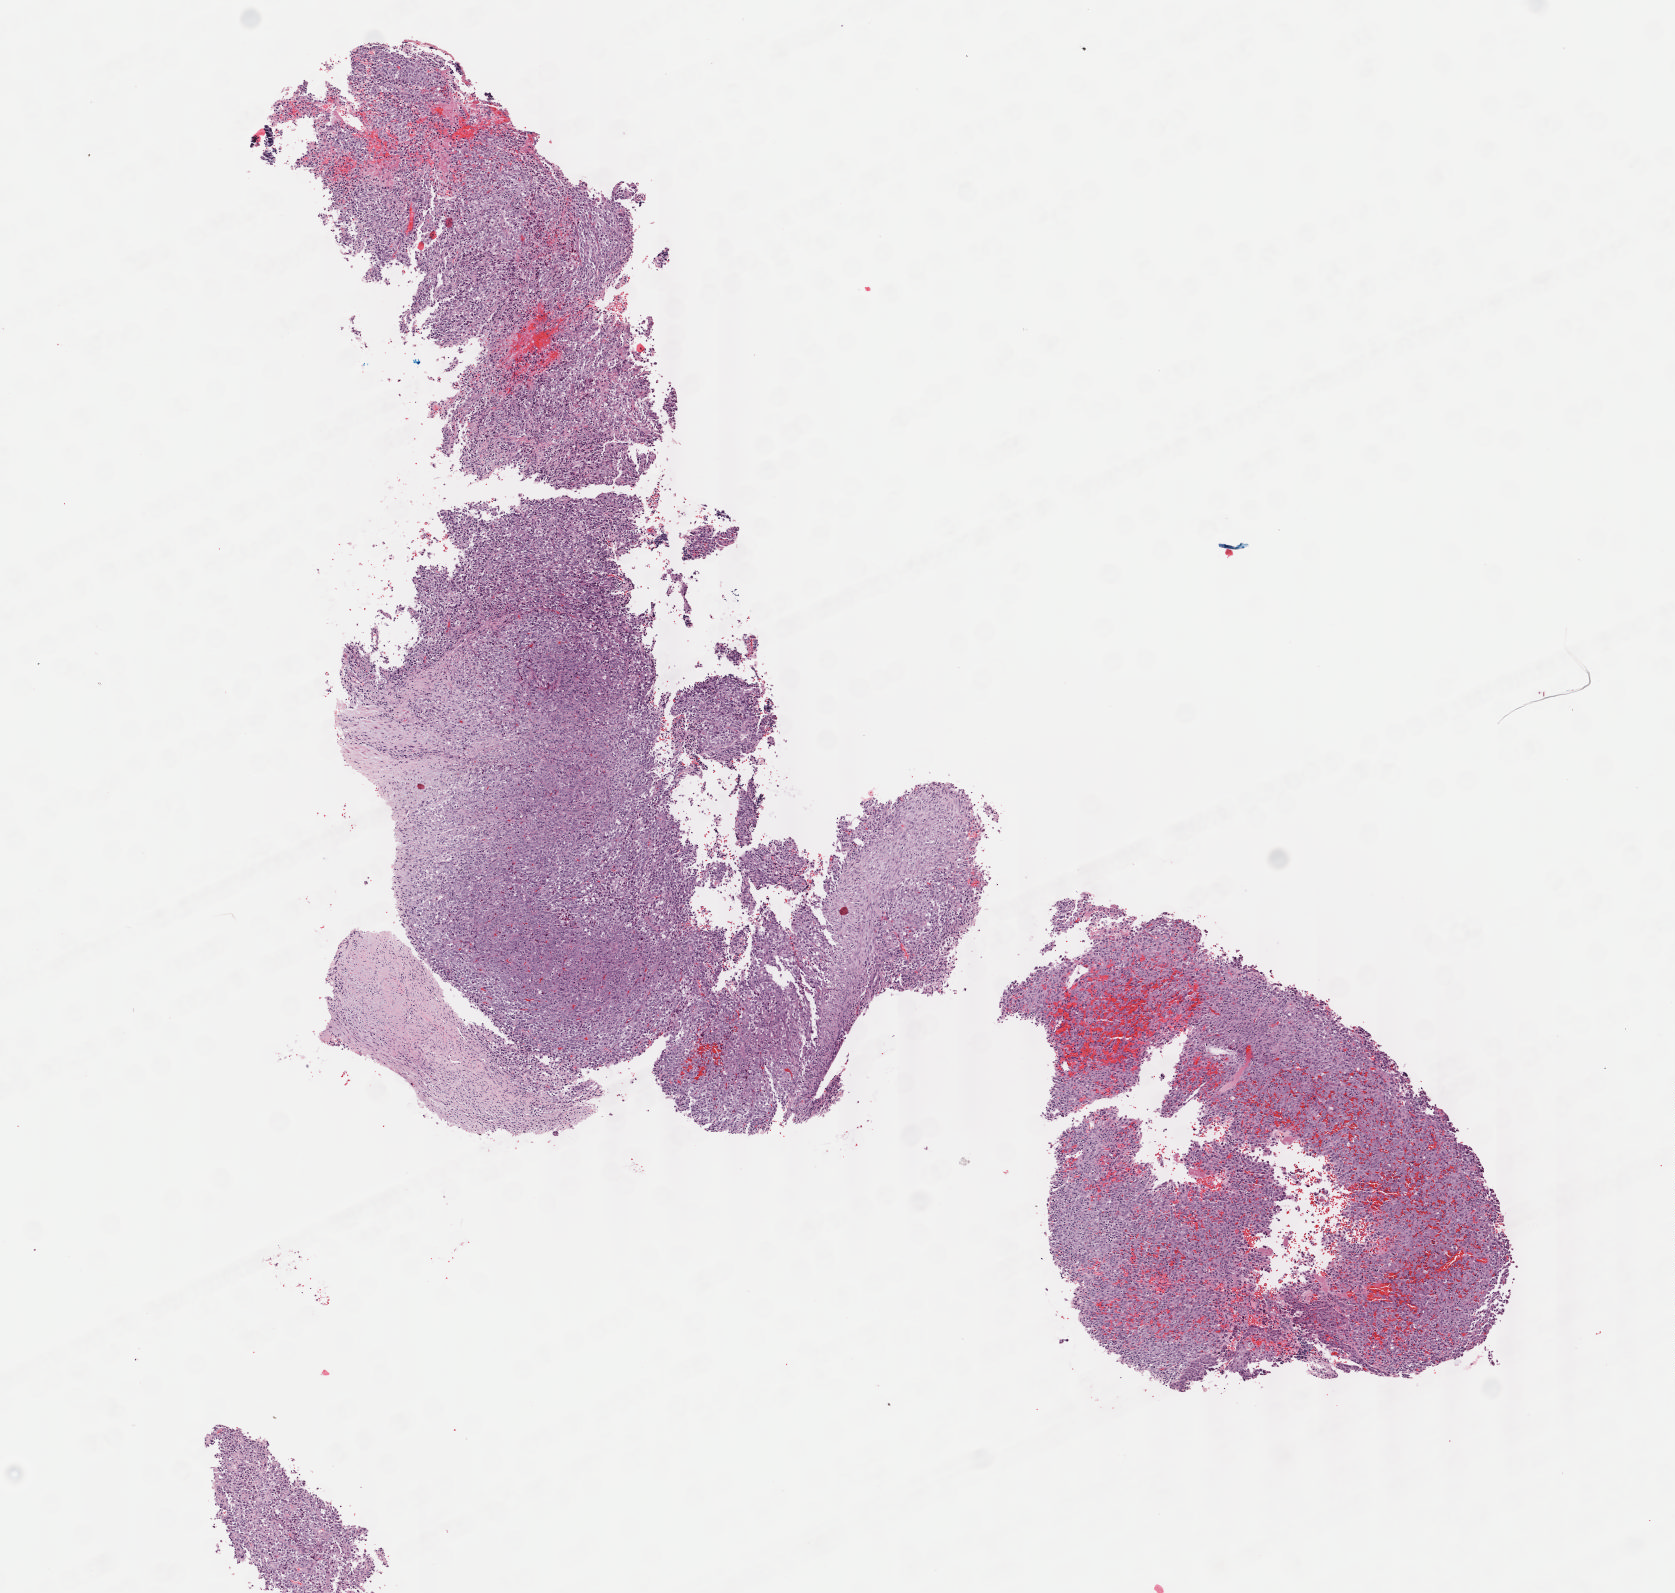
Hematoxylin and eosin (H&E) stained whole-slide image, low-resolution overview of the scanned area, about 6.7 x 6.3 mm (slide scanned at 40x), frozen section, bladder, primary tumour sample. Female patient; age at initial diagnosis 57 years.
Histologic diagnosis: Transitional cell carcinoma.